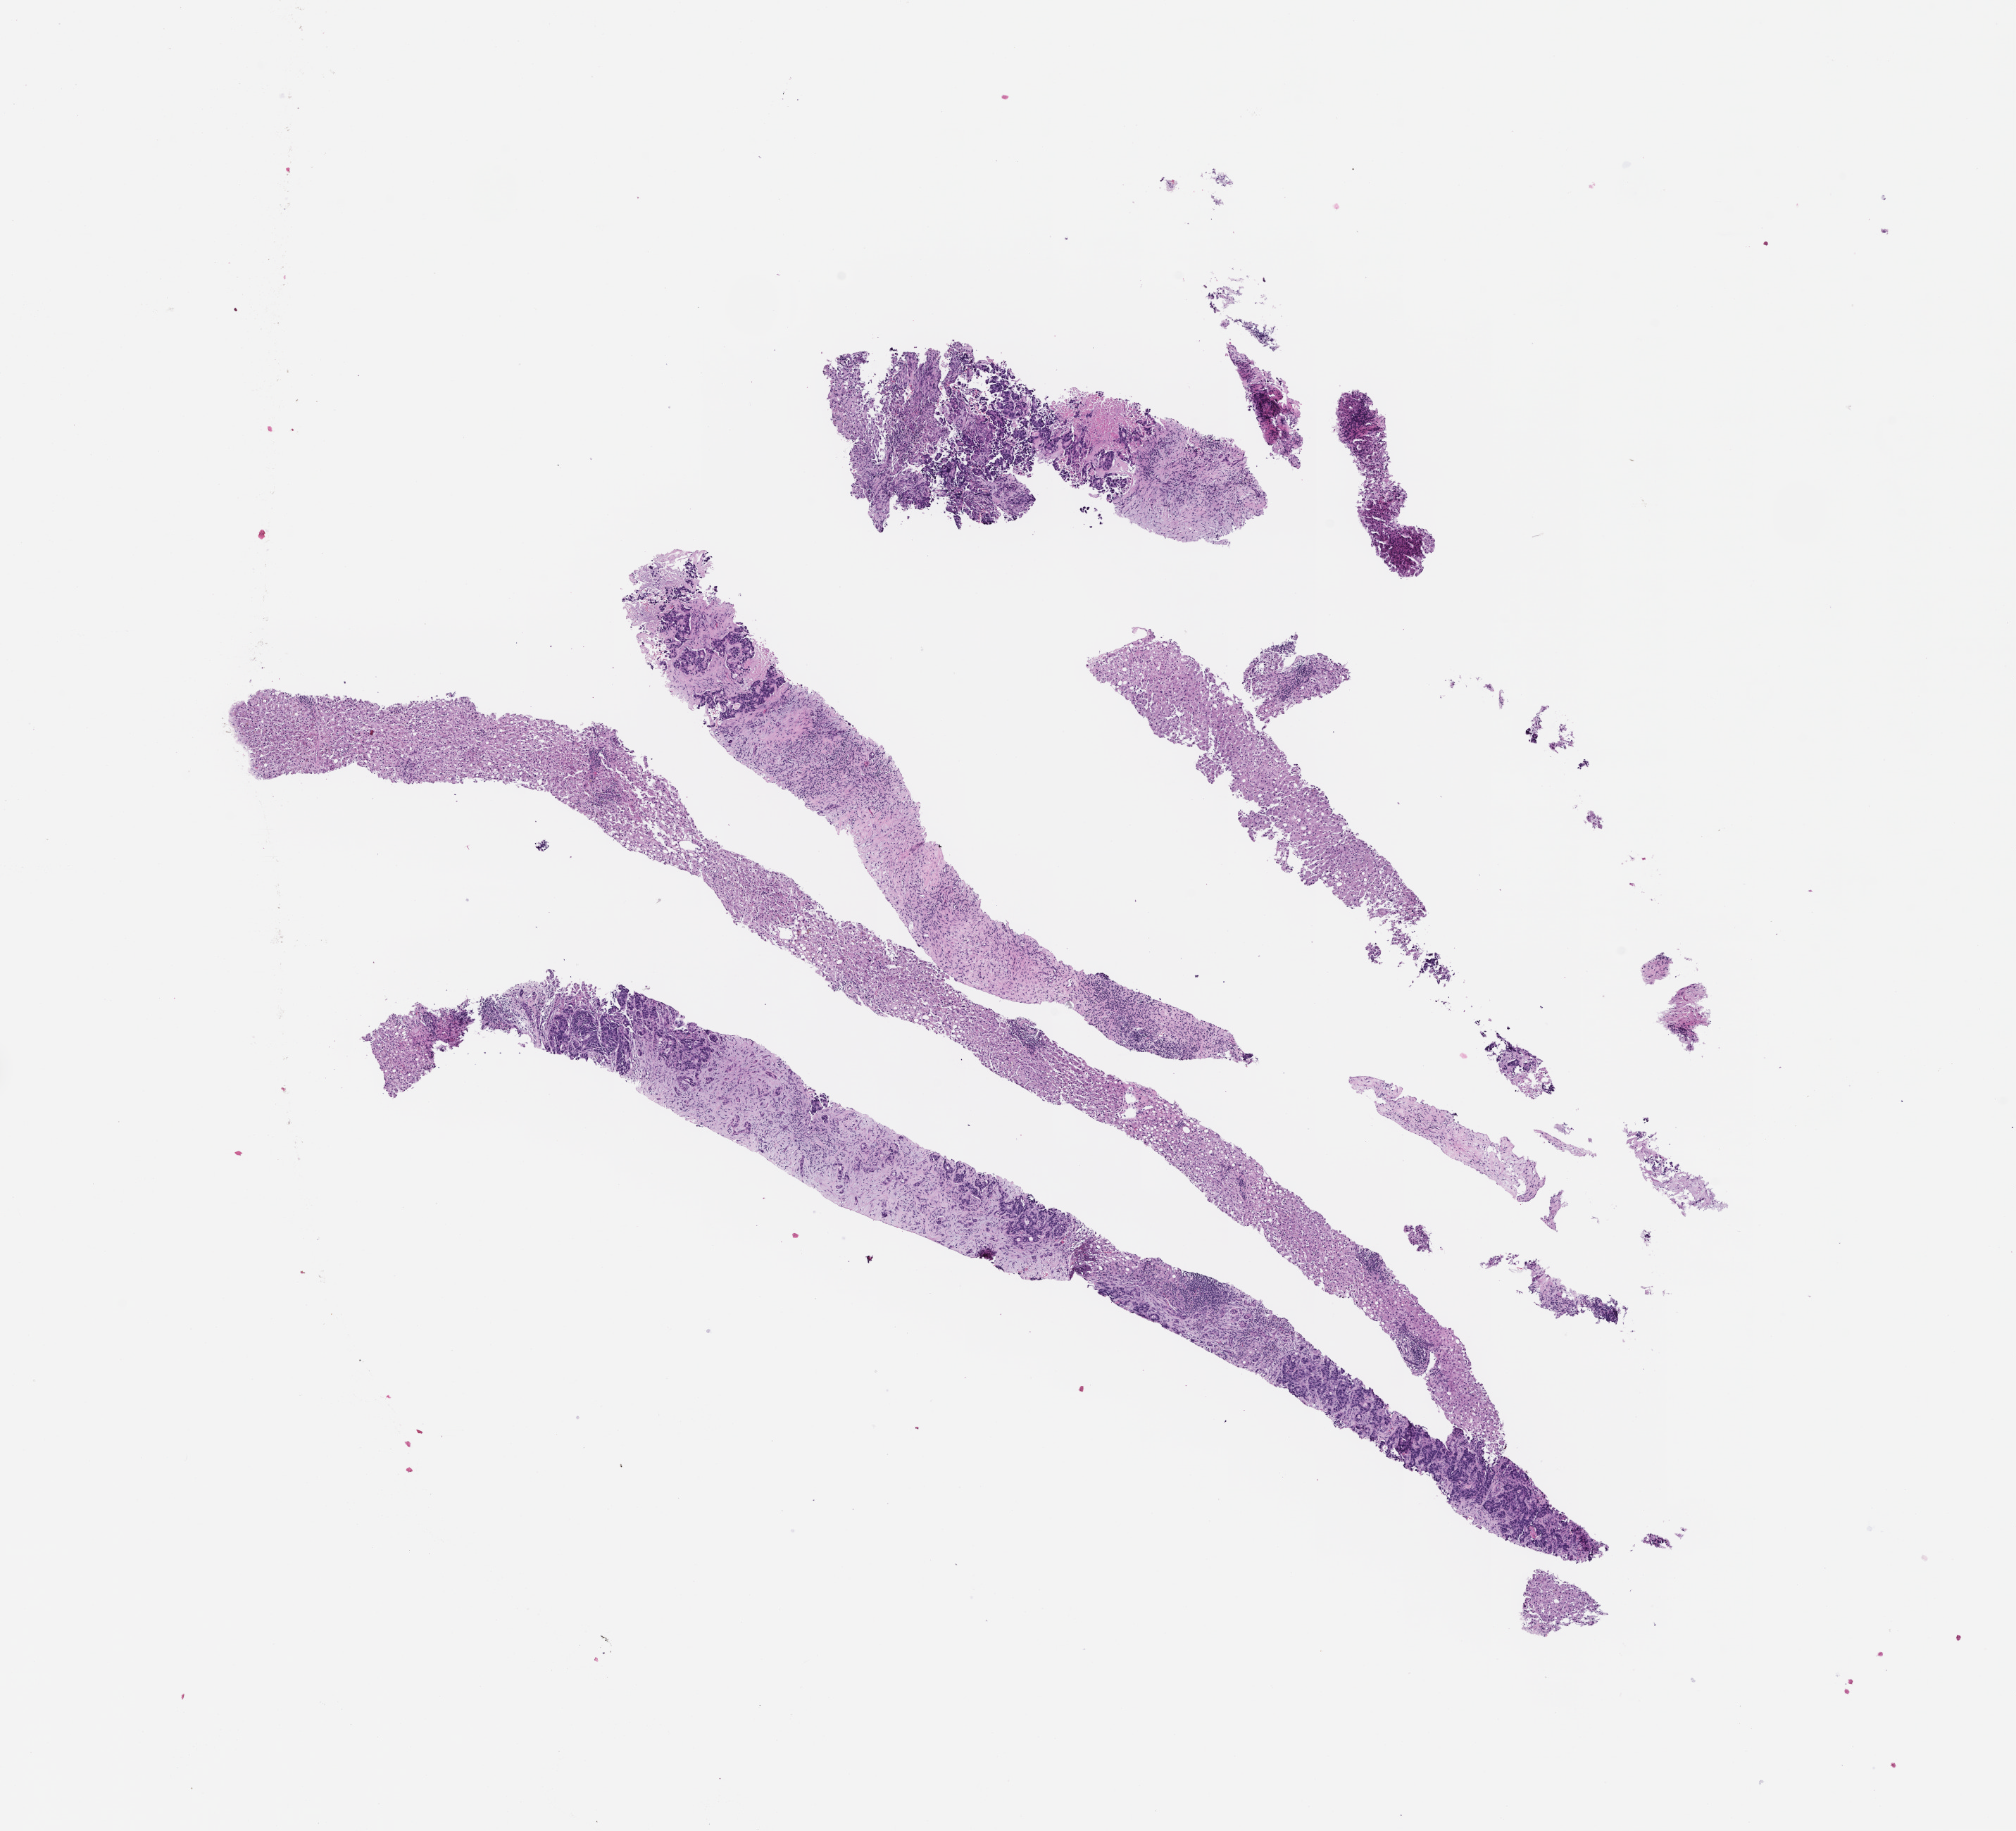
H&E whole-slide image — a low-resolution overview of the entire scanned area, about 11.6 x 10.5 mm; formalin-fixed, paraffin-embedded (FFPE) tissue; archival tissue. Patient sex: male.
This section: metastatic tumor tissue. Patient diagnosis (primary): Colorectal Carcinoma.